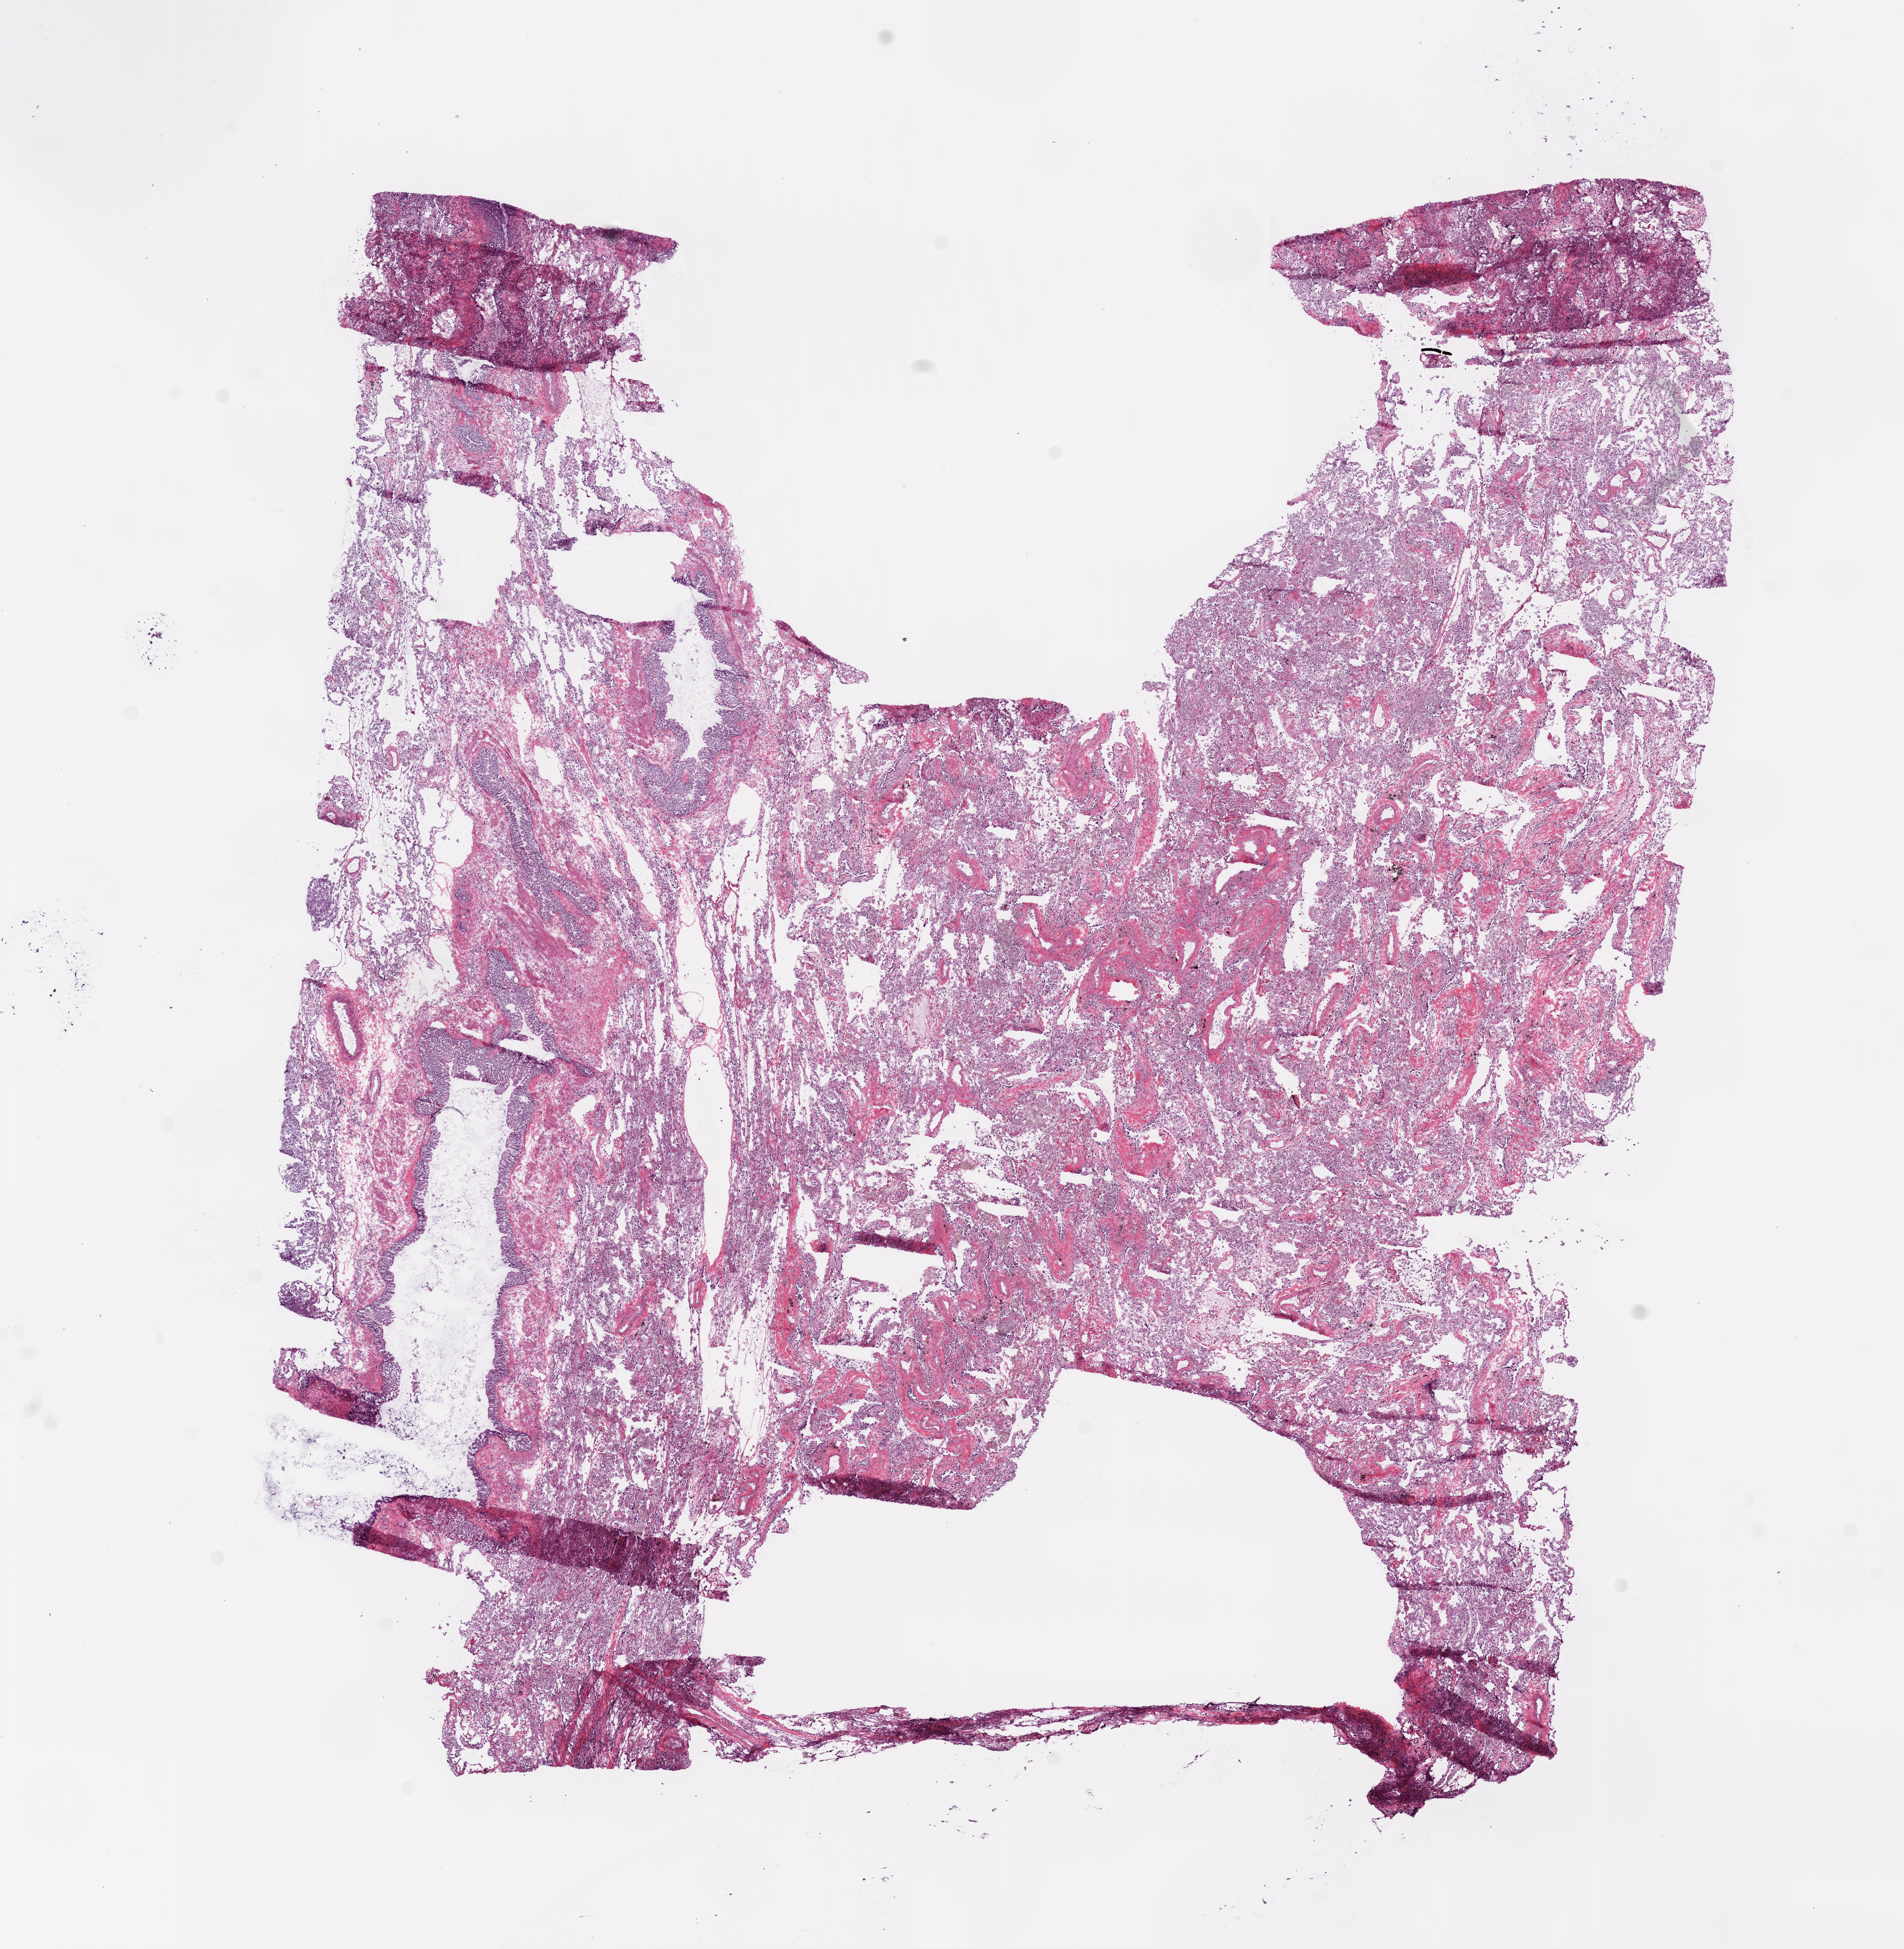
Digitized H&E-stained tissue section (whole slide), low-resolution overview of the scanned area, about 12.0 x 12.3 mm (from a 20x scan), frozen section from the bottom of the tissue portion, sample: solid tissue normal (non-tumour tissue), lung. Patient: female, age at initial diagnosis 47 years.
- this section: solid tissue normal sample (biorepository sample class)
- patient diagnosis: Squamous cell carcinoma, NOS